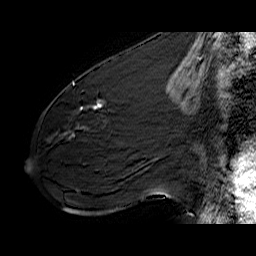
Breast MRI (dynamic contrast-enhanced), one sagittal slice; slice 32 of 60 in the series (ordered by position); dynamic contrast-enhanced series, time point 2 of 6 at this slice position (early post-contrast); 1.5 T; TE 6.4 ms, TR 32.9 ms; 256 × 256 image matrix, field of view 200 × 200 mm. Female patient. Case-level facts recorded for this patient, not image findings: setting: breast cancer imaged before/during neoadjuvant chemotherapy; receptor status: HER2-positive.
Structures marked on this image (semi-automatically segmented with operator editing):
- analysis volume of interest (the breast-tissue region the enhancement analysis was run in; not a lesion): bounding box <61,77,141,142> (left, top, right, bottom; pixels)
- tumour enhancement mask (voxels above the 100 % enhancement threshold inside the analysis volume of interest): <73,82,102,110>